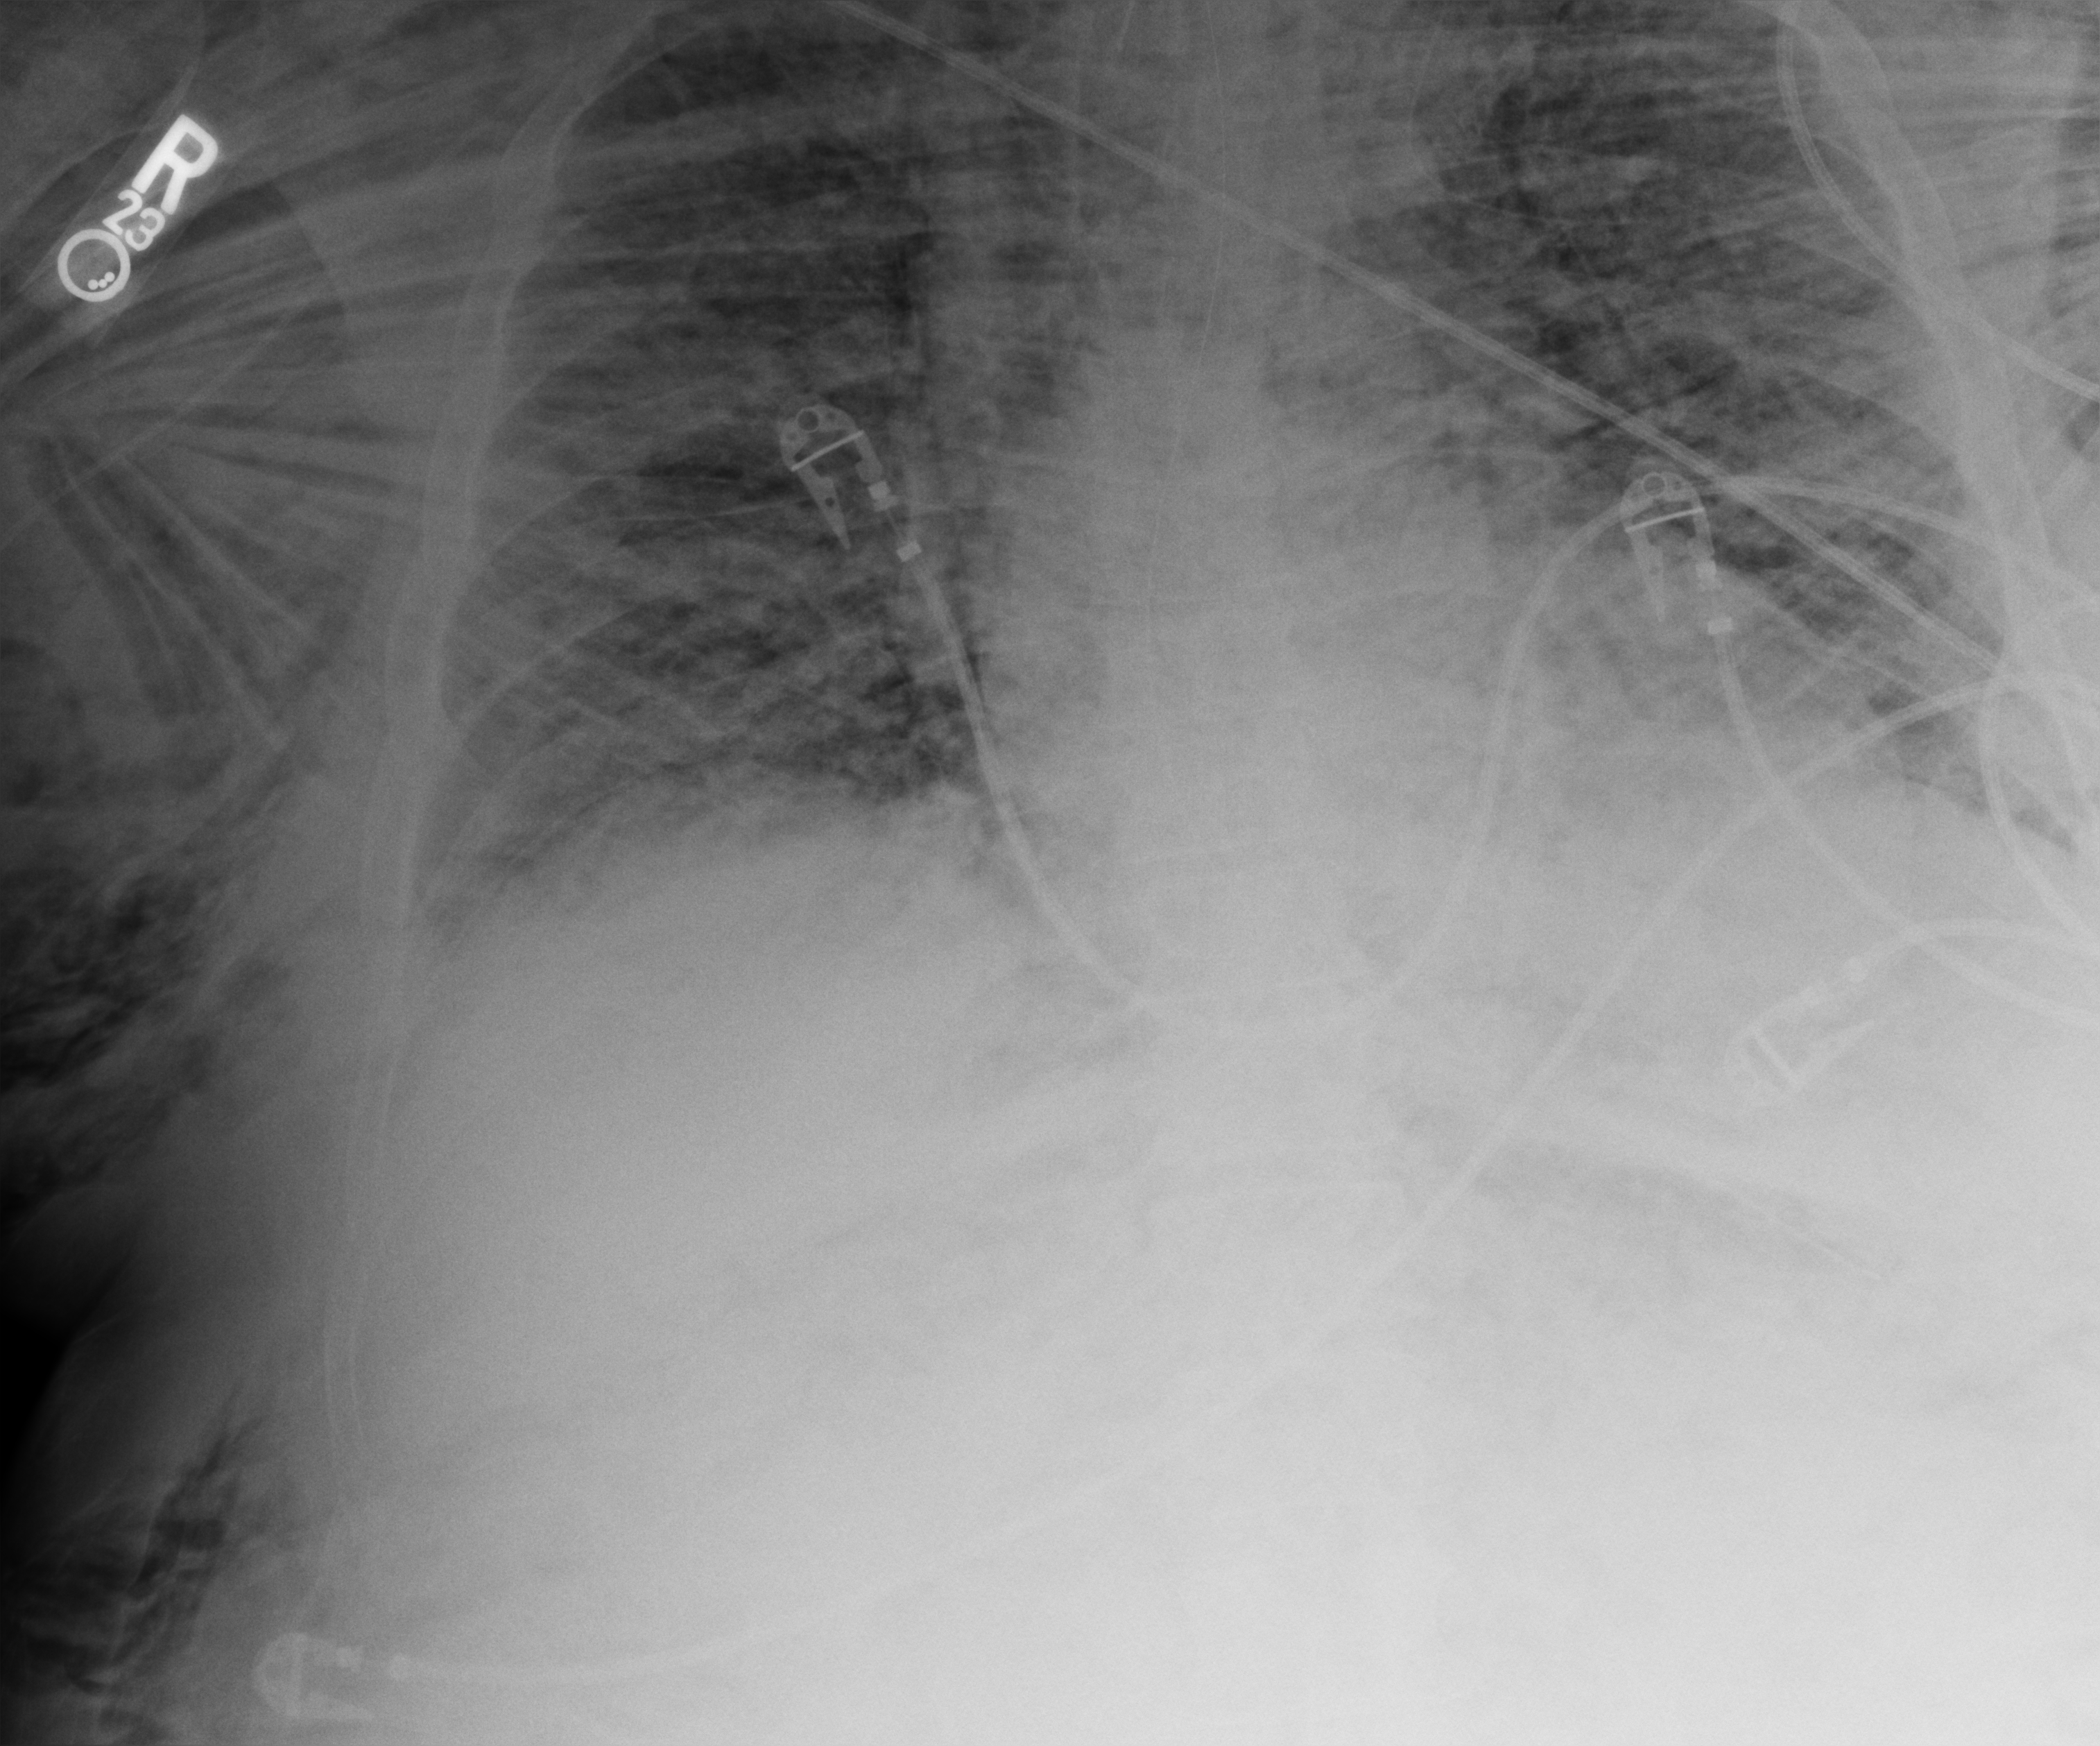
Bedside chest radiograph (computed radiography), anteroposterior (AP) projection. Patient hospitalised with COVID-19, aged 18–59 years.
Hospital-stay facts (about this admission, not read from this image; timing relative to this image not recorded): mechanically ventilated during this hospital stay: yes; admitted to intensive care during this hospital stay: yes.